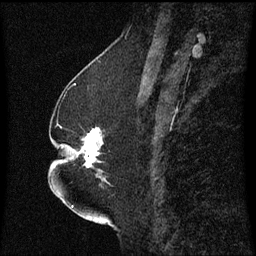
Breast MRI (dynamic contrast-enhanced), one sagittal slice; slice 25 of 60 in the series (ordered by position); dynamic contrast-enhanced series, image 2 of 3 at this slice position (ordered by acquisition); 1.5 T; TE 4.2 ms, TR 8.4 ms; 256 × 256 image matrix, field of view 200 × 200 mm. Patient: female, 52 years. From the clinical record (not read from this slice): setting: breast cancer imaged before/during neoadjuvant chemotherapy; receptor status: HR-positive, HER2-negative.
Outlined on this slice (semi-automatic segmentation, software-assisted and operator-edited):
- analysis volume of interest (the breast-tissue region the enhancement analysis was run in; not a lesion): bounding box <65,128,111,183> (left, top, right, bottom; pixels)
- tumour enhancement mask (voxels above the 70 % enhancement threshold inside the analysis volume of interest): <80,130,103,167>